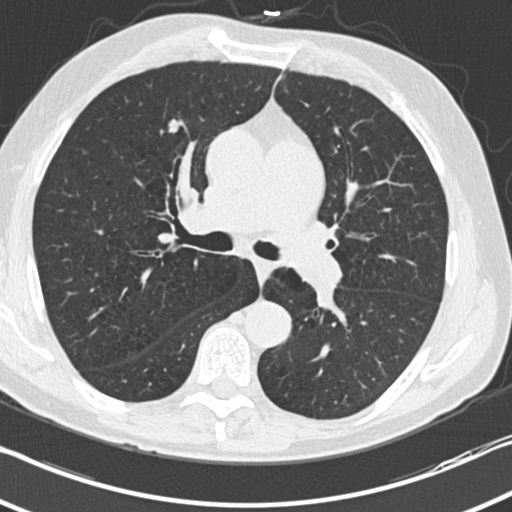
Low-dose screening chest CT, one axial slice; position 127 of 212 along the scan axis; lung window (W 1500 / L -600 HU); 512 × 512 image matrix.
Outlined on this slice (expert manual segmentation):
- lesion 1 (tumor, upper lobe of right lung): bounding box <169,119,180,133> (left, top, right, bottom; pixels)